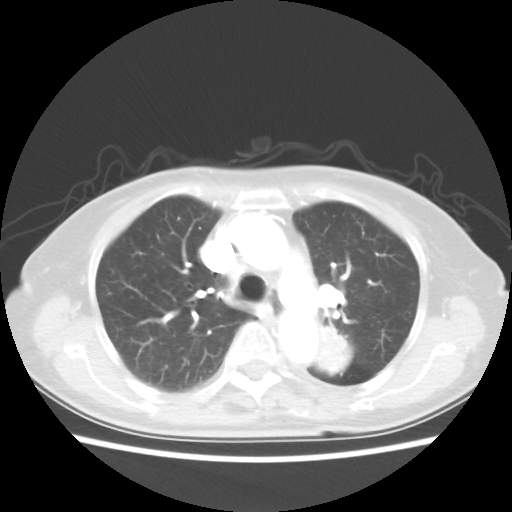
Chest CT, one axial slice; position 33 of 50 along the scan axis; reconstruction kernel STANDARD; 80 kVp; lung window (W 1500 / L -600 HU); 5 mm slice thickness; 512 × 512 image matrix. Female patient, age 81 years. Case-level facts recorded for this patient, not image findings: clinical TNM (as recorded): T2 N0 M1a.
Annotated regions visible in this slice (rectangle marked by the reading radiologist):
- lung tumour (recorded histology: squamous cell carcinoma): box from (x=316, y=319) to (x=360, y=388) px